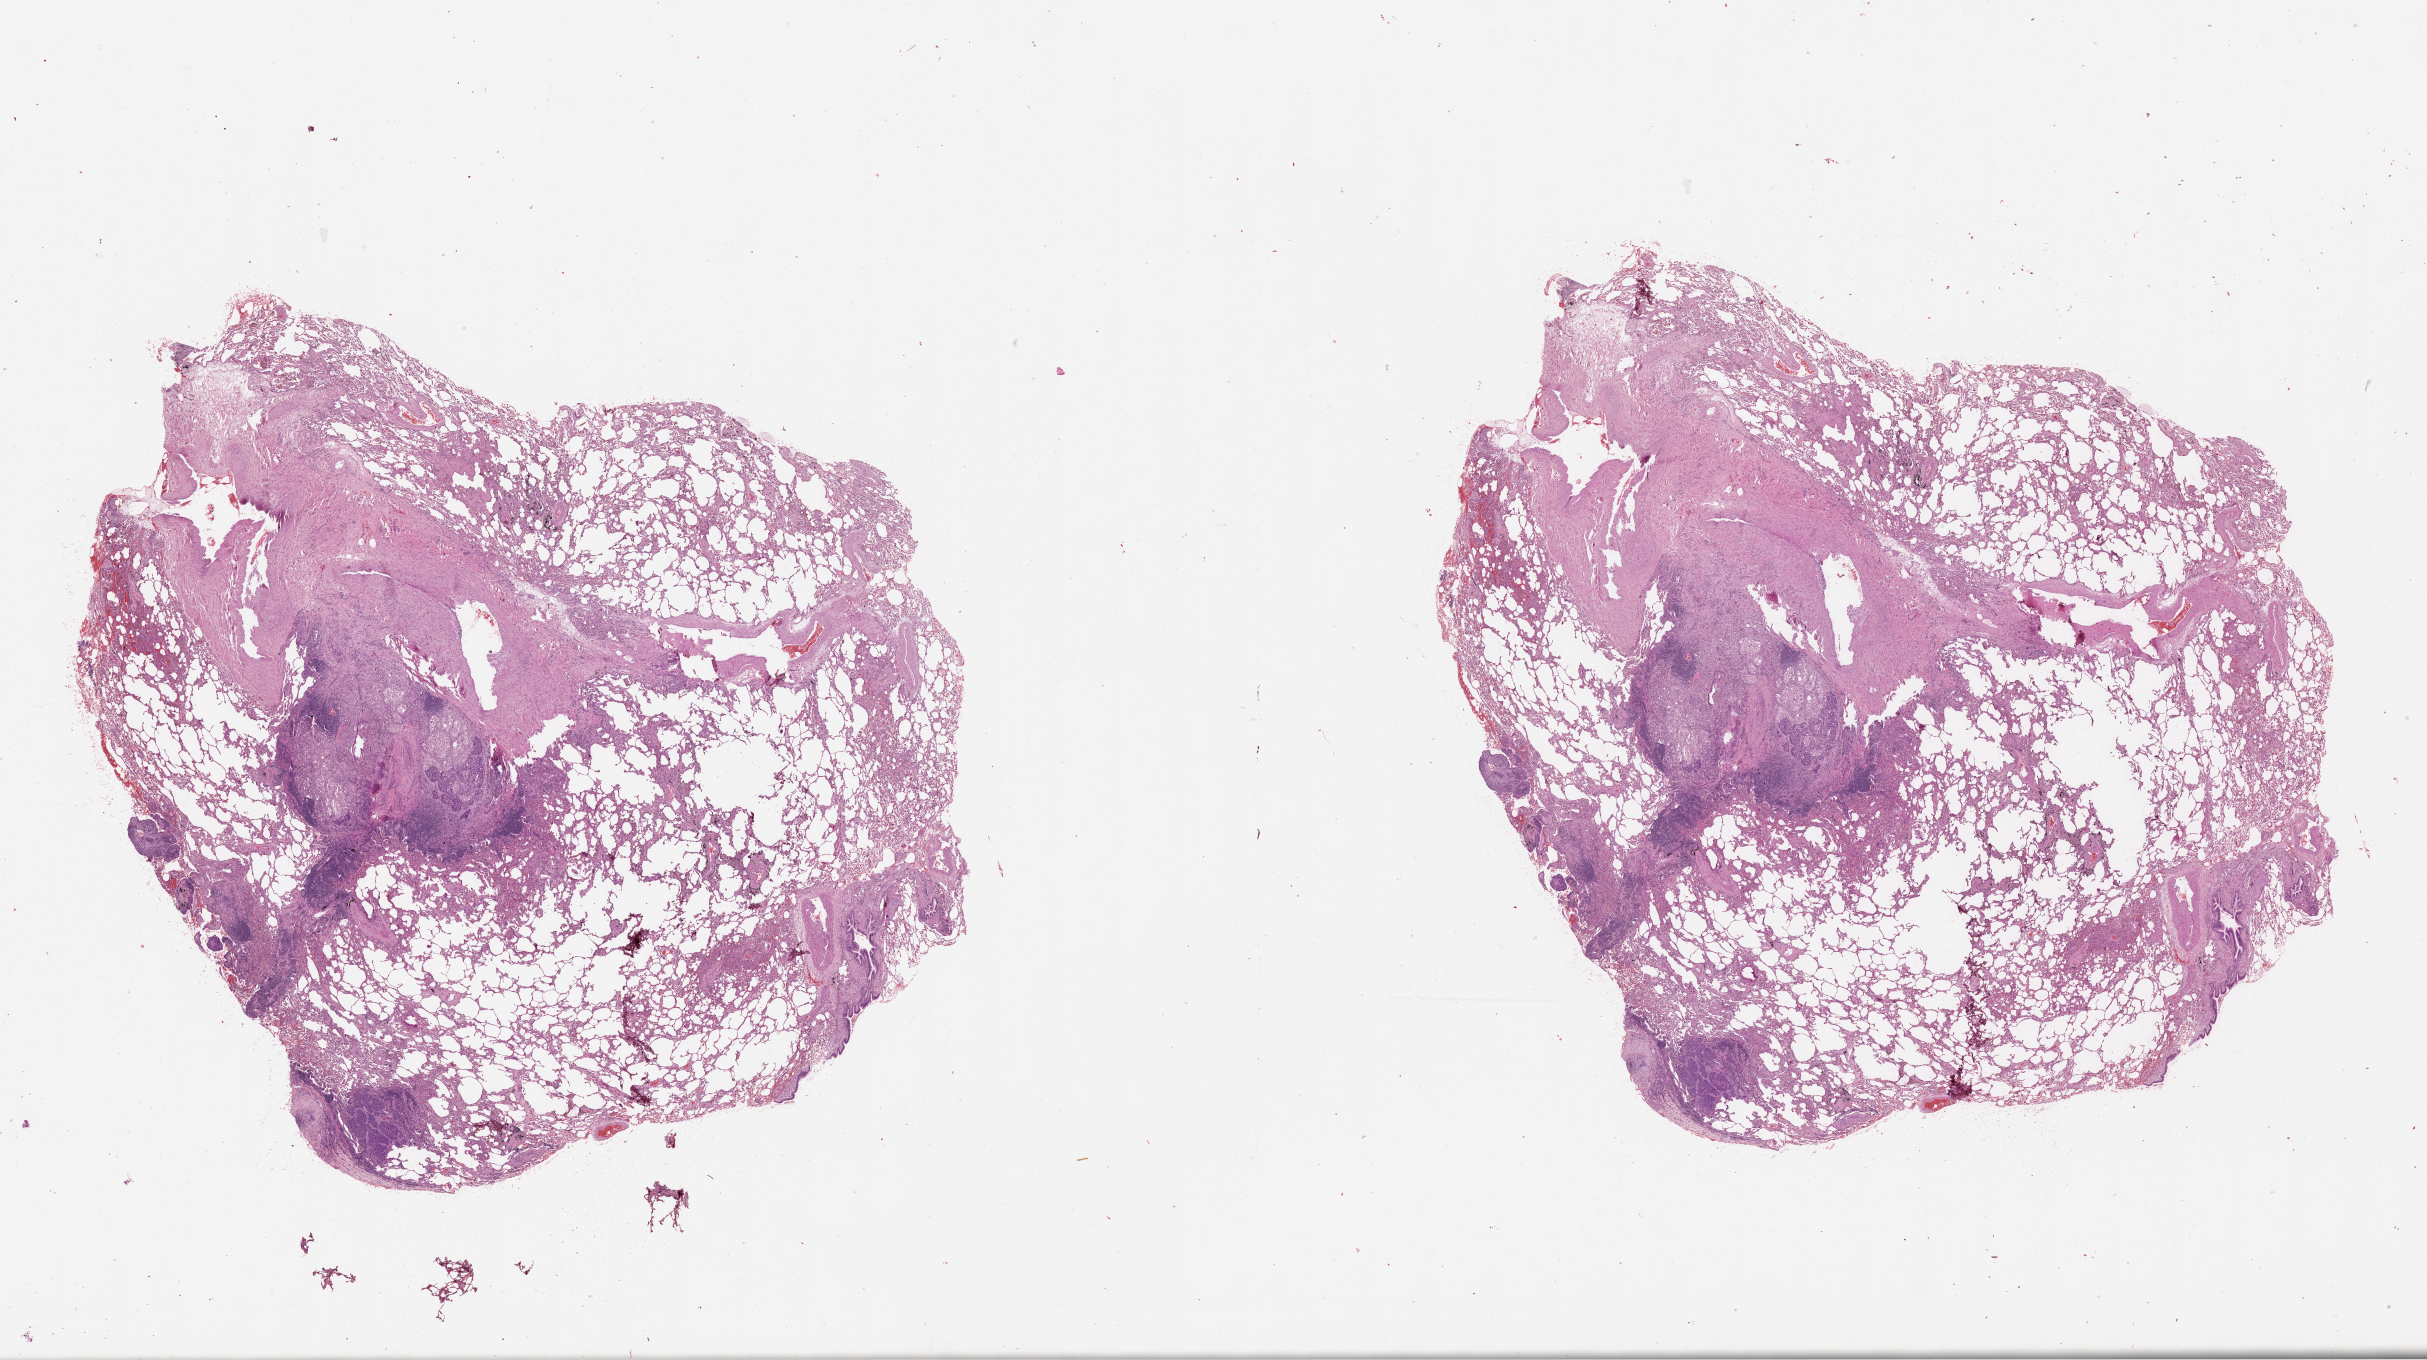
Hematoxylin and eosin (H&E) stained whole-slide image — whole scanned area (about 39.1 x 21.9 mm) shown as a low-resolution overview, lung, tumour tissue. Patient: male, age 59 years.
• patient diagnosis (cohort enrolment): squamous cell carcinoma (lung)